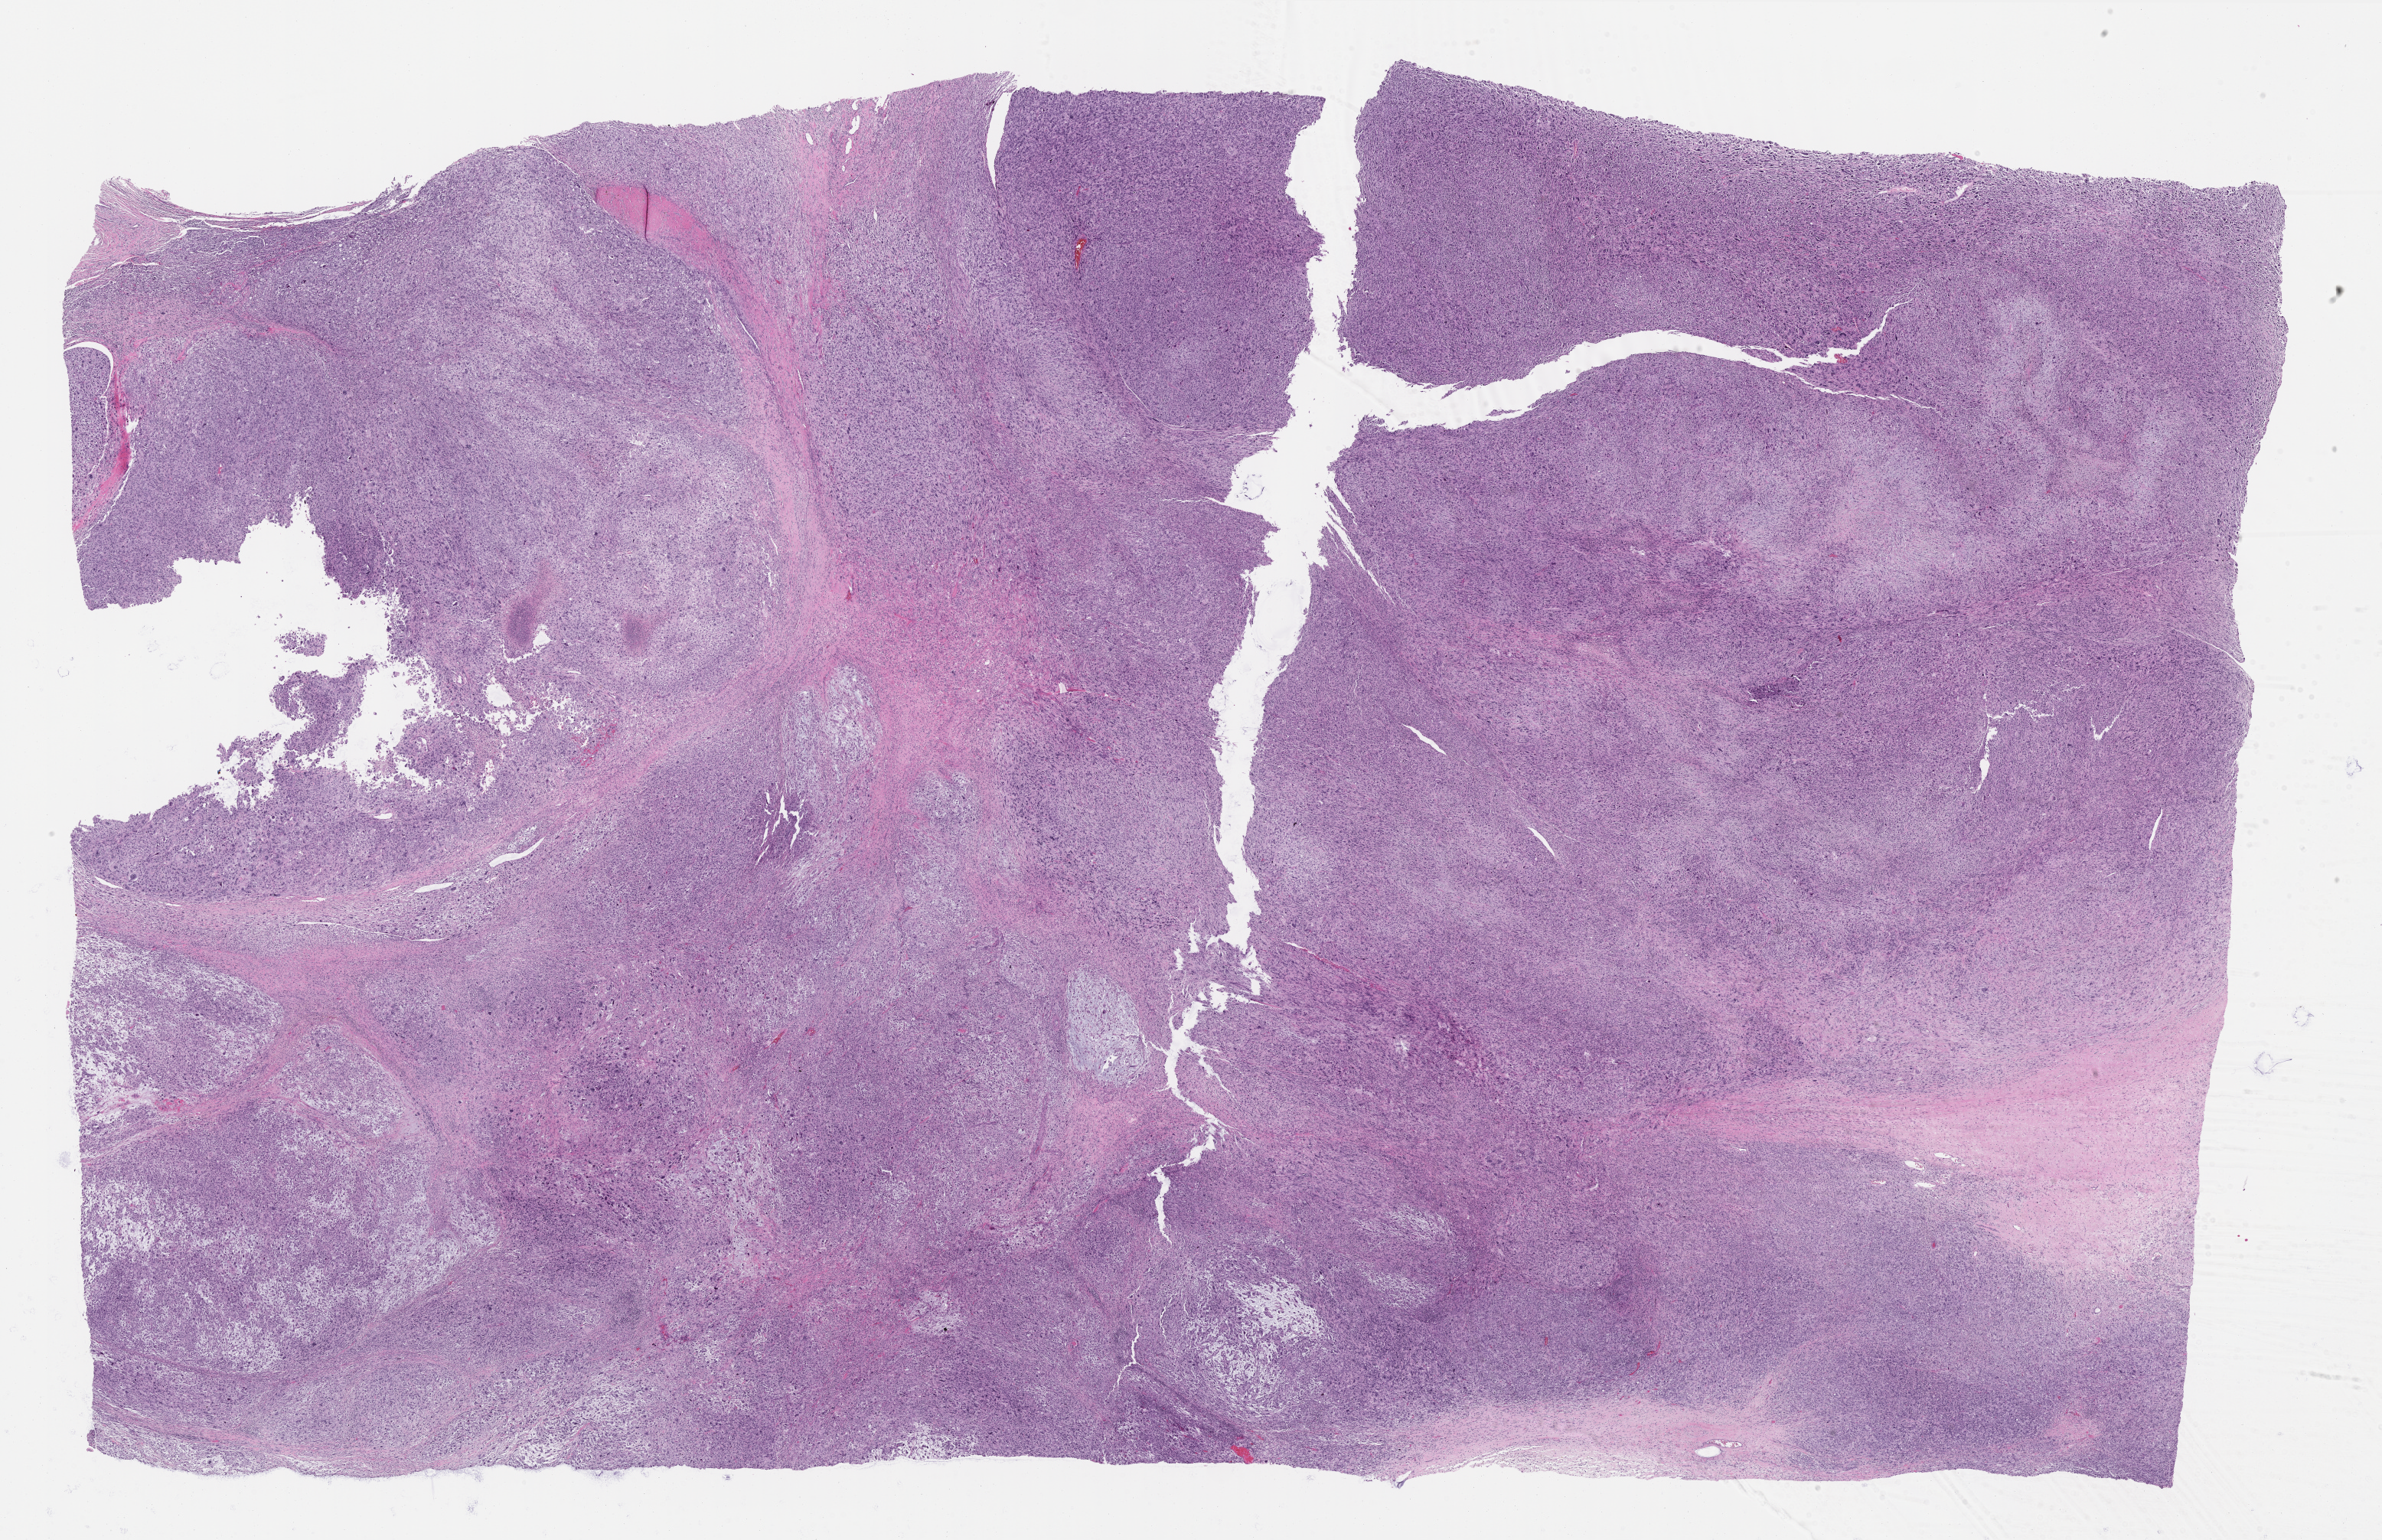
H&E whole-slide image — shown as a low-resolution overview of the whole scanned area (about 25.0 x 16.2 mm, slide scanned at 40x); formalin-fixed paraffin-embedded (FFPE) diagnostic section; primary tumour sample from the connective, subcutaneous and other soft tissues. Male, age 86 years at initial diagnosis.
Pathologic diagnosis: Undifferentiated sarcoma (connective, subcutaneous and other soft tissues of trunk, NOS).